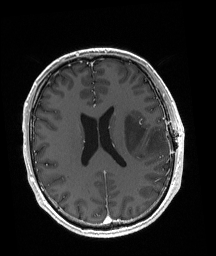
Brain MRI from a brain-tumour surgery series, one axial slice; T1-weighted post-contrast; 1 mm slice thickness; 216 × 256 image matrix, field of view 211 × 250 mm. From the clinical record (not read from this slice): histopathology: Astrocytoma; WHO grade: 3; IDH mutation: yes; tumour location: Left Posterior Frontal.
Annotated regions visible in this slice (expert manual segmentation):
- tumour: bounding box <125,113,167,154> (left, top, right, bottom; pixels)